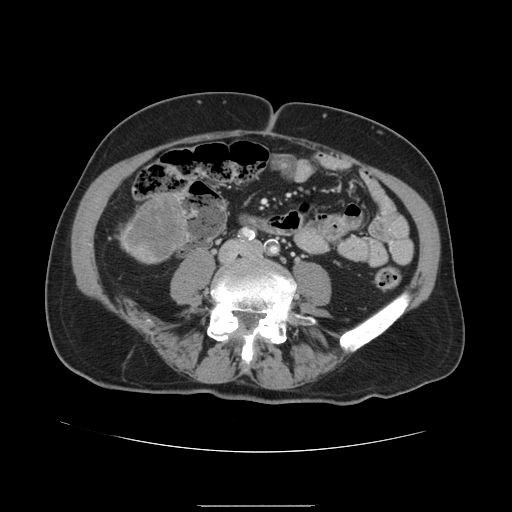
Contrast-enhanced abdominal CT, one axial slice; position 12 of 168 along the scan axis; soft-tissue window (W 400 / L 40 HU); 2.5 mm slice thickness; 512 × 512 image matrix, field of view 386 × 386 mm. Male patient, age 74 years. Case-level facts recorded for this patient, not image findings: diagnosis: colorectal cancer liver metastases, imaged before liver resection; multiple liver metastases: no.
Outlined on this slice (manually delineated by an expert):
- liver: bounding box <122,192,189,265> (left, top, right, bottom; pixels)
- liver metastasis: <125,195,187,260>